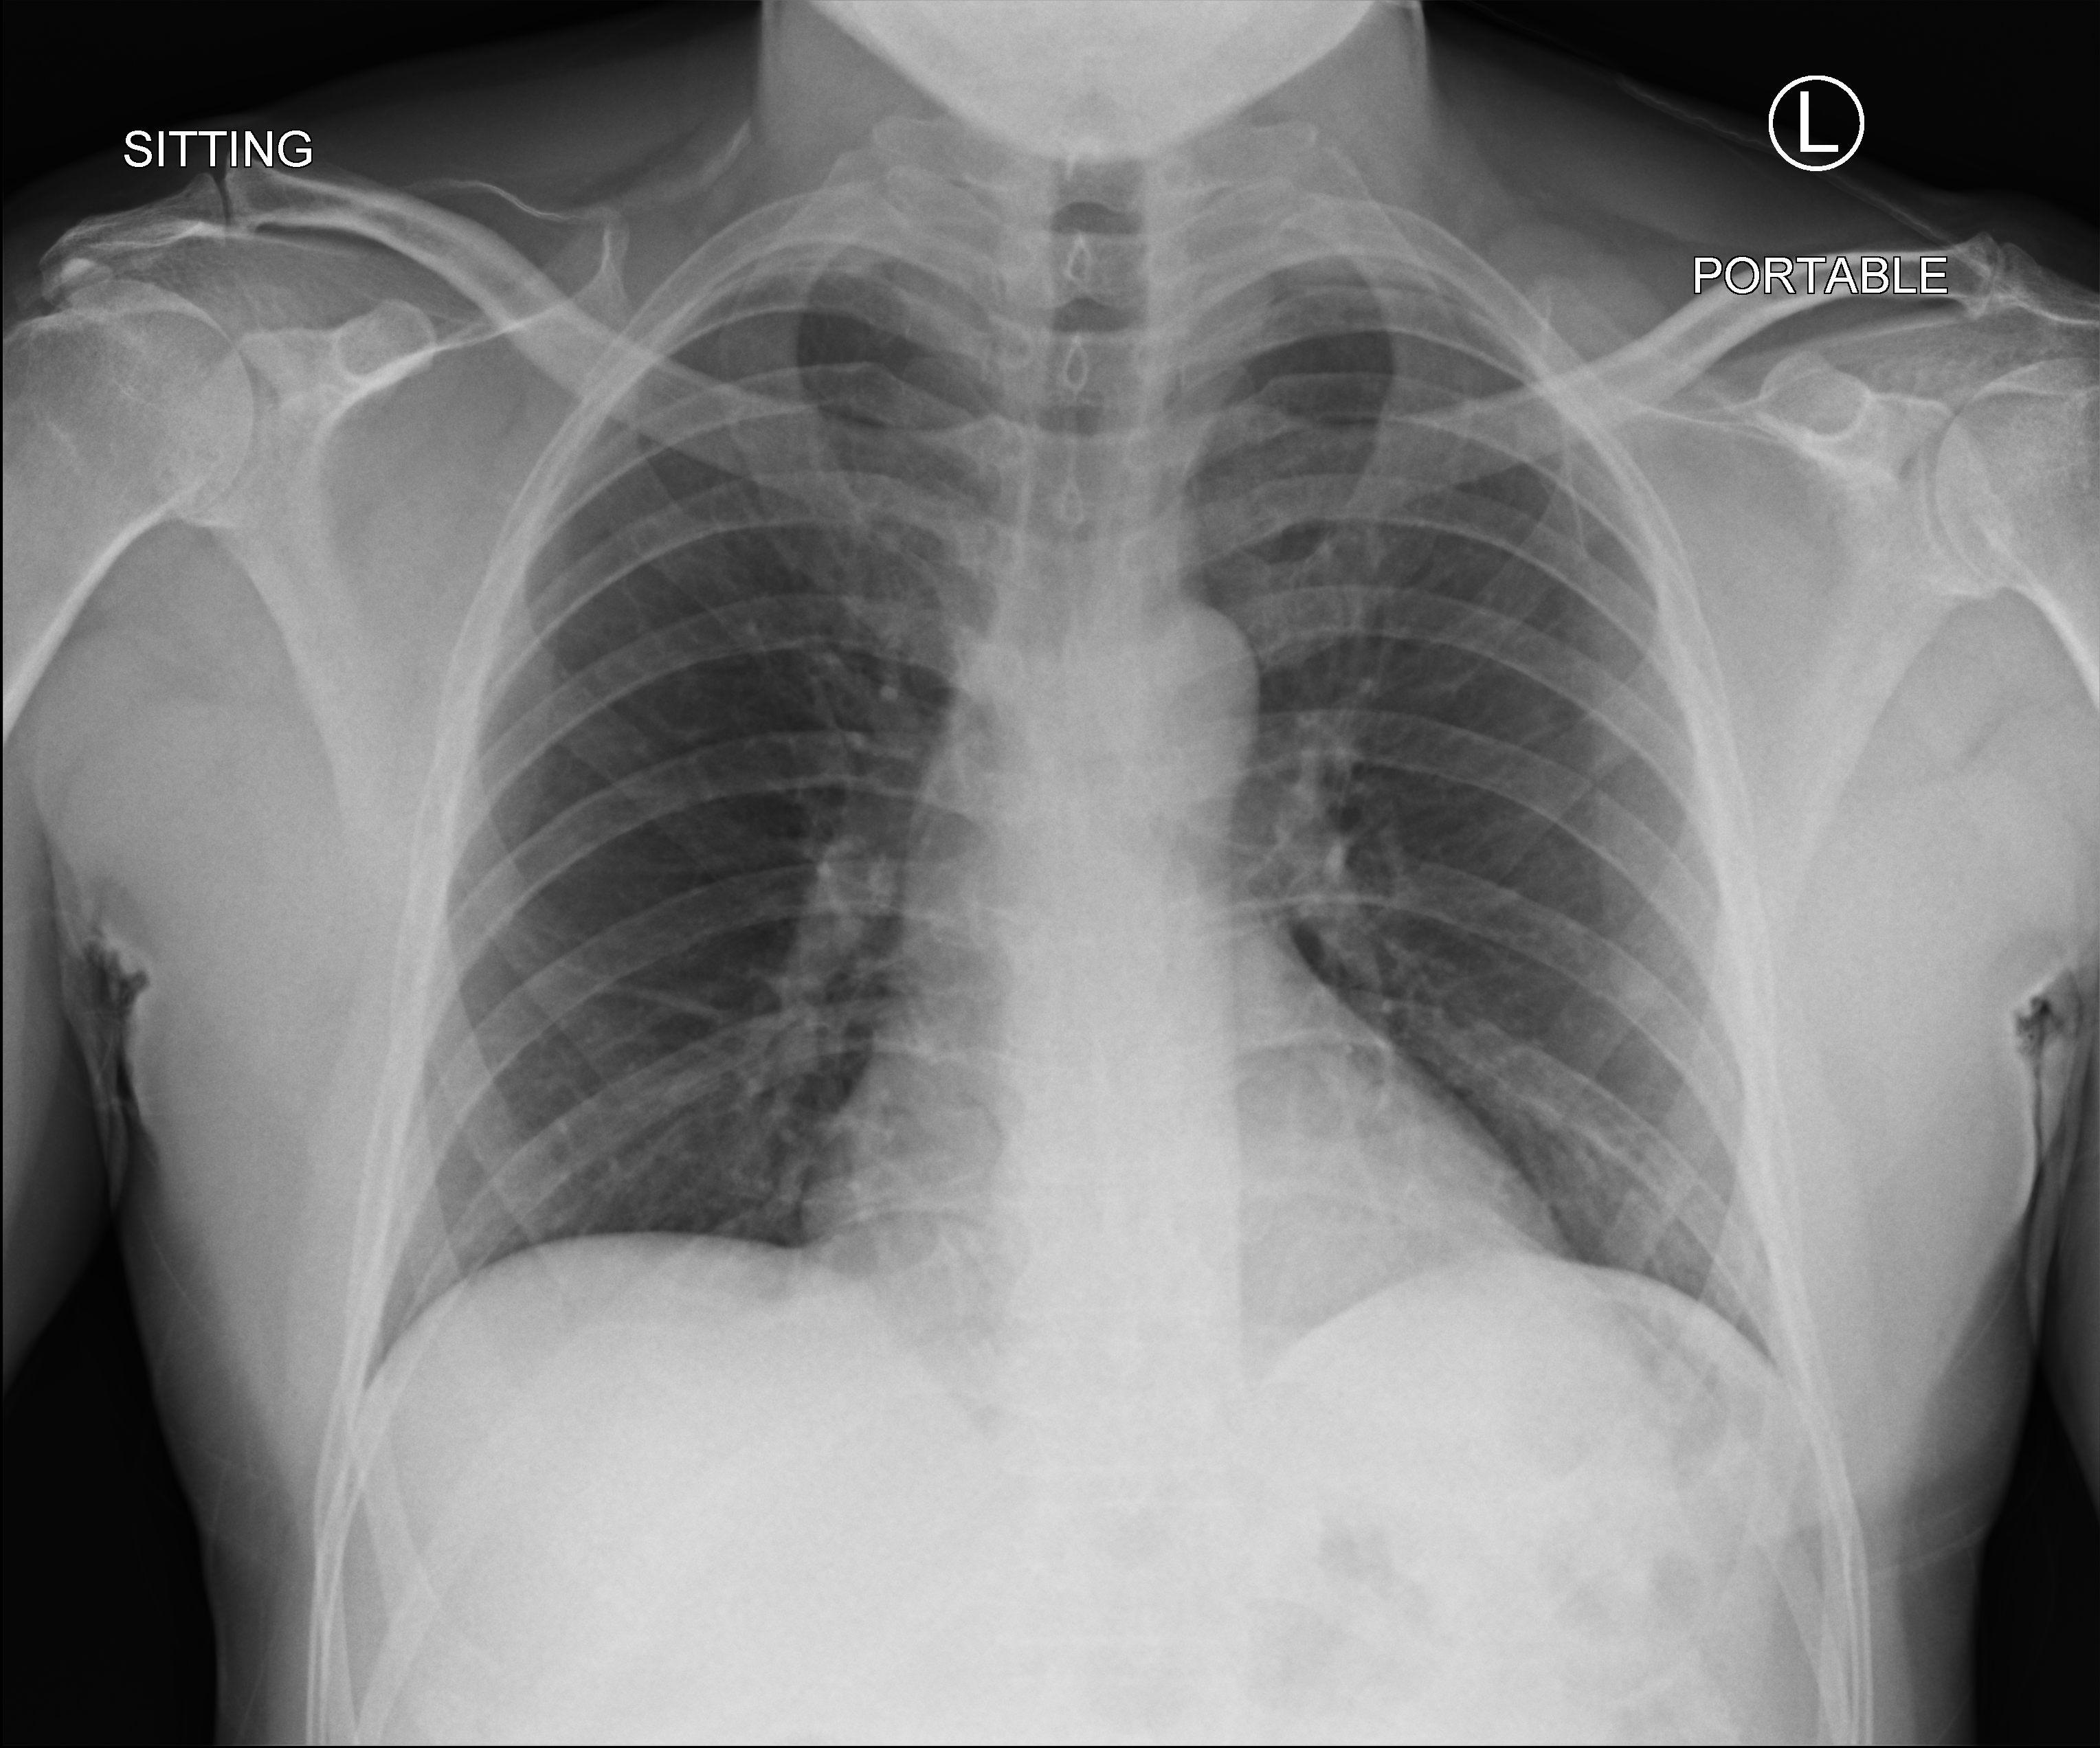
Portable chest radiograph. Male patient hospitalised with COVID-19, age 18–59 years.
From the hospital-stay record, not from the radiograph (when in the stay this image was taken is not recorded): admitted to intensive care during this hospital stay: no.